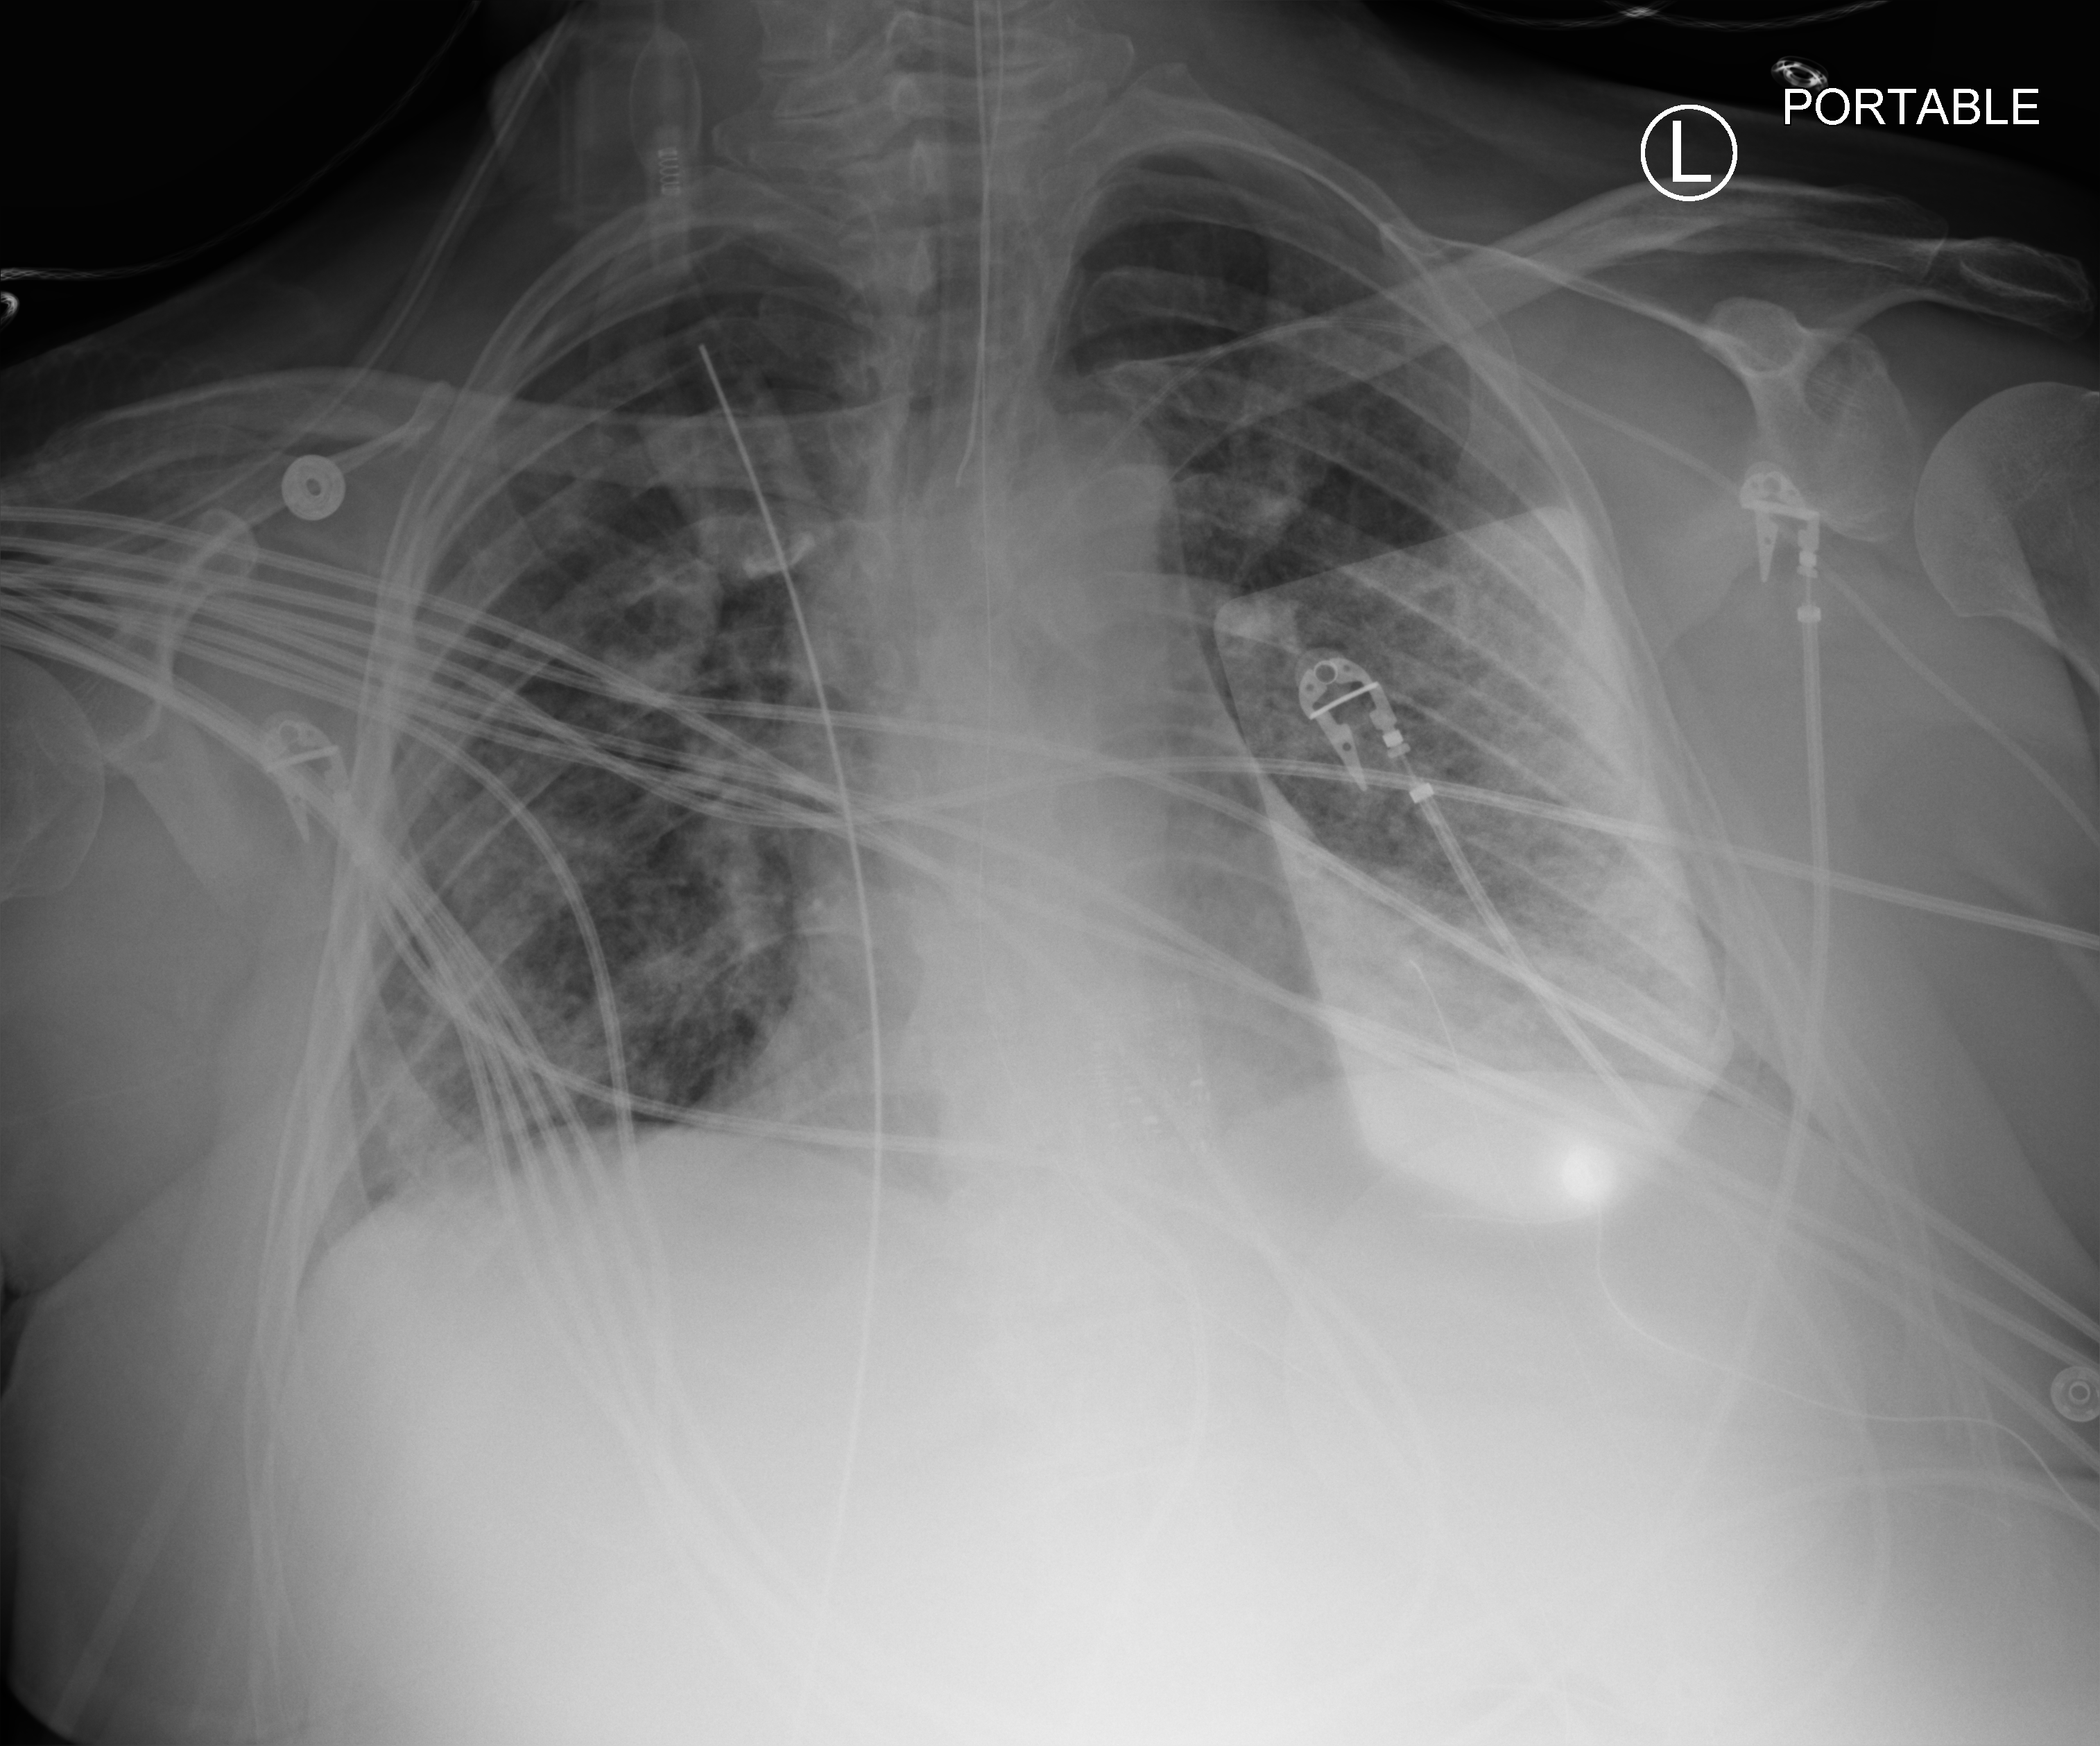
Bedside chest radiograph (computed radiography); anteroposterior (AP) projection. Male patient hospitalised with COVID-19, age 18–59 years.
Hospital-stay facts (about this admission, not read from this image; timing relative to this image not recorded):
- diabetes (admission record): no
- COPD (admission record): no